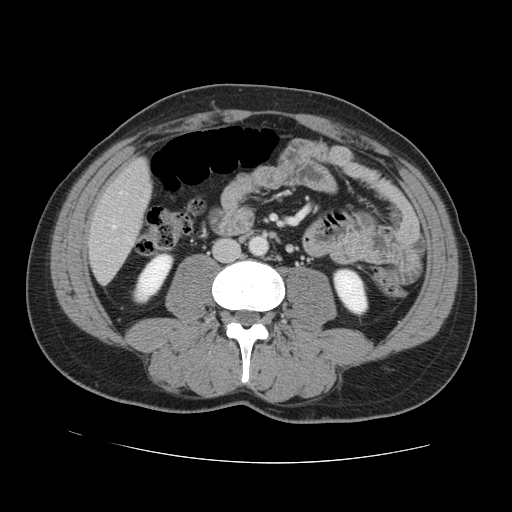
Contrast-enhanced abdominal CT, one axial slice; position 26 of 131 along the scan axis; intravenous contrast given; soft-tissue window (W 400 / L 40 HU); 512 × 512 image matrix, field of view 380 × 380 mm. Male patient, age 40 years. From the clinical record (not read from this slice): diagnosis: colorectal cancer liver metastases, imaged before liver resection; multiple liver metastases: yes; largest metastasis: 2.9 cm.
Annotated regions visible in this slice (manually delineated by an expert):
- hepatic veins: bounding box (x1, y1, x2, y2) in pixels: (112, 192, 121, 229)
- liver: (90, 161, 150, 282)